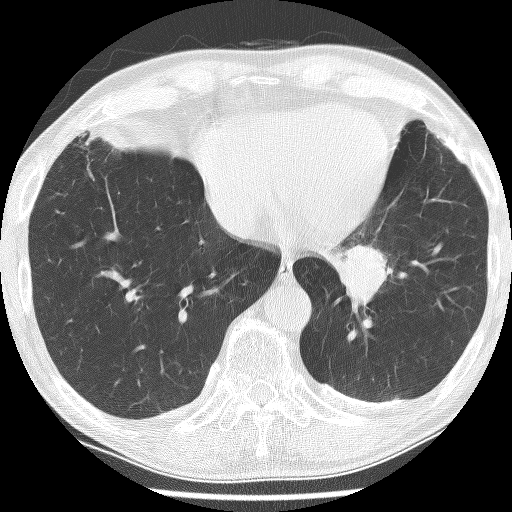
Low-dose screening chest CT, one axial slice. Position 51 of 226 along the scan axis. Reconstruction kernel BONE. Lung window (W 1500 / L -600 HU). 512 × 512 image matrix.
Annotated regions visible in this slice (manually delineated by an expert):
- lesion 1 (tumor, lower lobe of left lung): bounding box [x1, y1, x2, y2] px = [339, 245, 389, 313]